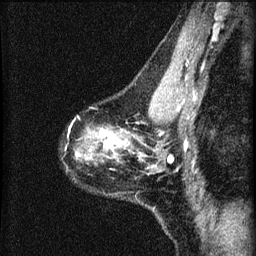
Breast MRI (dynamic contrast-enhanced), one sagittal slice; position 40 of 60 along the scan axis; dynamic contrast-enhanced series, image 2 of 4 at this slice position (ordered by acquisition); 1.5 T; TE 4.2 ms, TR 8.2 ms; 2 mm slice thickness; 256 × 256 image matrix, field of view 180 × 180 mm. Patient: female, 41 years.
Annotated regions visible in this slice (semi-automatically segmented with operator editing):
- analysis volume of interest (the breast-tissue region the enhancement analysis was run in; not a lesion): bounding box <70,91,166,210> (left, top, right, bottom; pixels)
- tumour enhancement mask (voxels above the 70 % enhancement threshold inside the analysis volume of interest): <78,128,128,159>